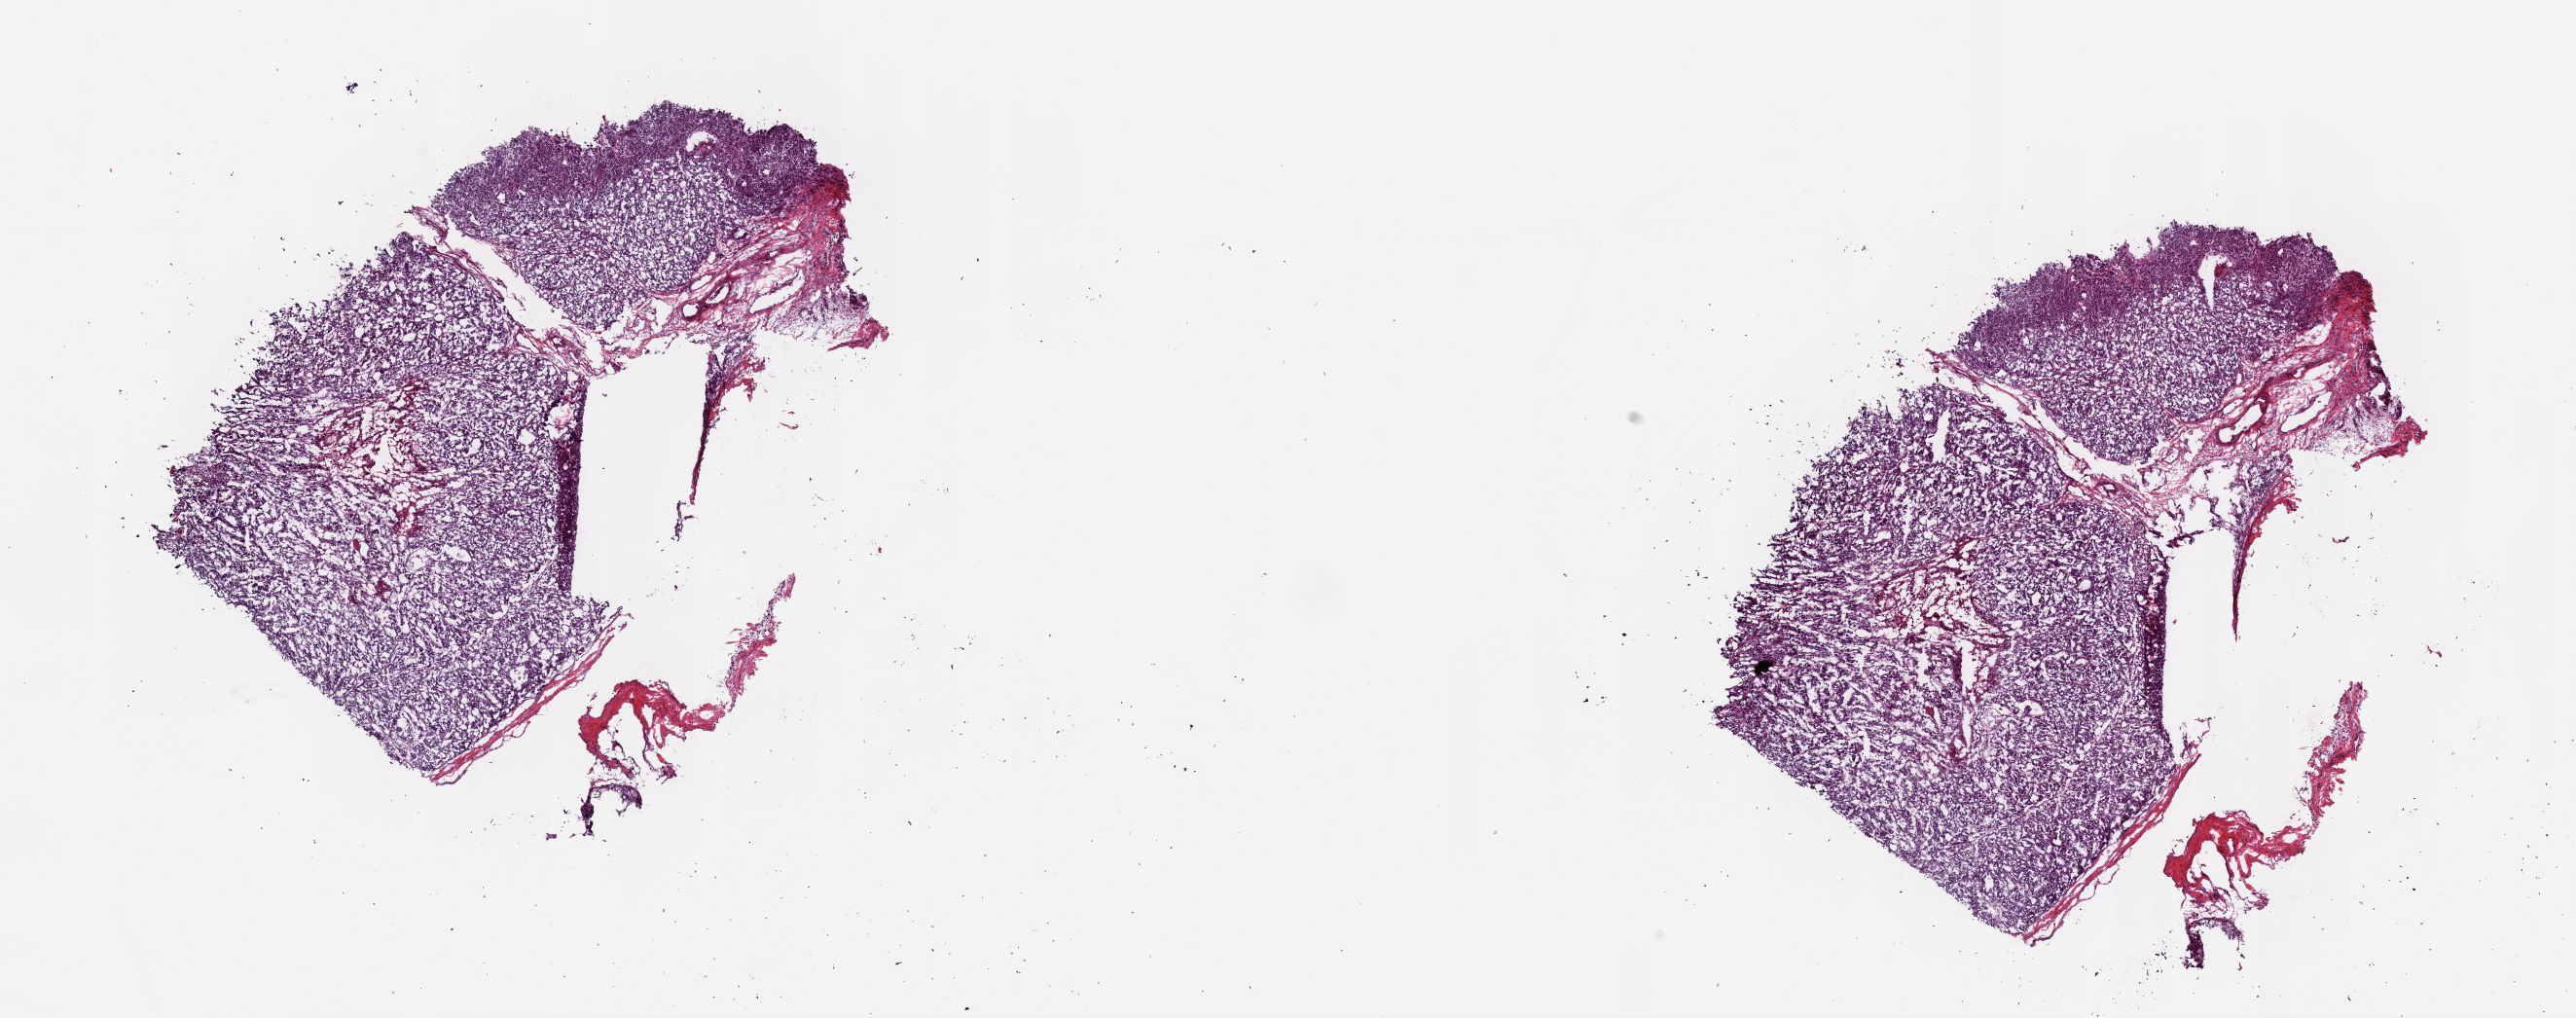
Digitized H&E tissue section (whole slide), low-resolution overview of the scanned area, about 20.9 x 8.3 mm (slide scanned at 40x), frozen section from the top of the tissue portion, metastatic tumour sample, sampled site not recorded. Female, age 54 years at initial diagnosis. Slide review estimates, as recorded: tumour cells 85%, tumour nuclei 90%, normal cells 10%, stromal cells 0%, necrosis 5%. Inflammatory infiltration, as recorded: lymphocyte infiltration 2%, monocyte infiltration 2%, neutrophil infiltration 0%.
* this section: metastatic tumour tissue
* patient diagnosis: Malignant melanoma, NOS